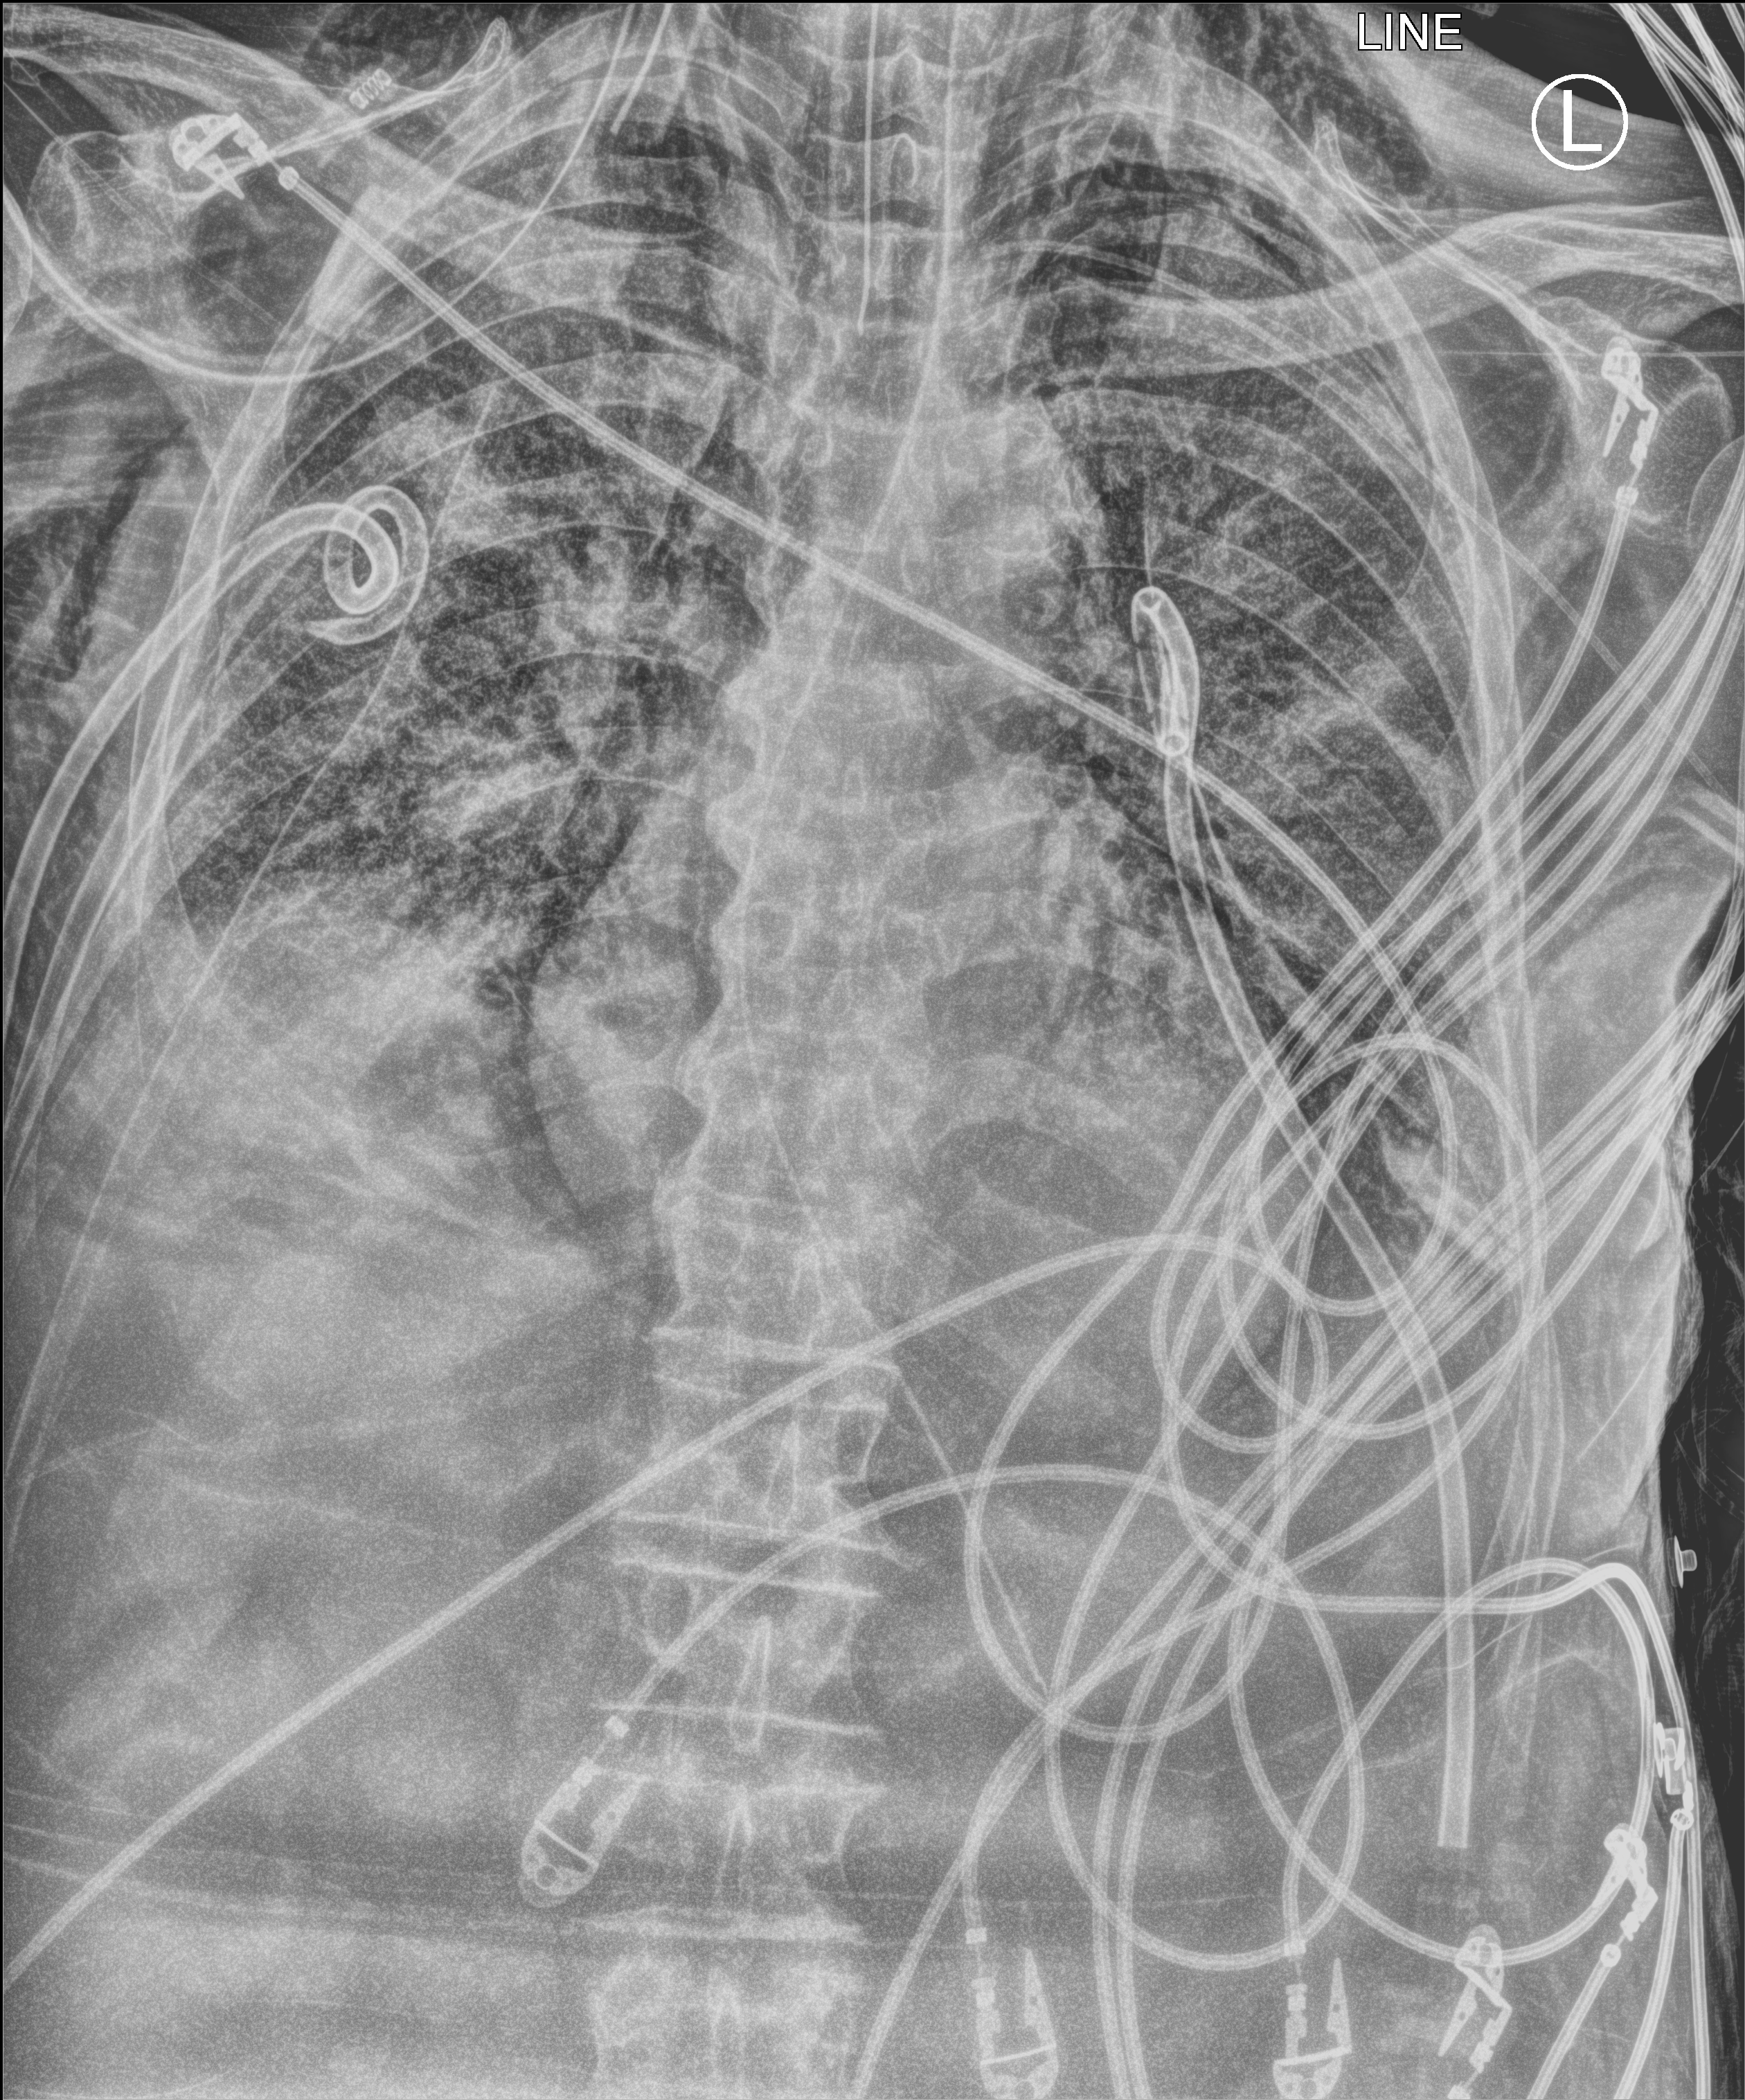
Portable chest radiograph; anteroposterior (AP) projection. Male patient hospitalised with COVID-19, age 75–90 years.
Hospital-stay facts (about this admission, not read from this image; timing relative to this image not recorded):
- admitted to intensive care during this hospital stay: yes